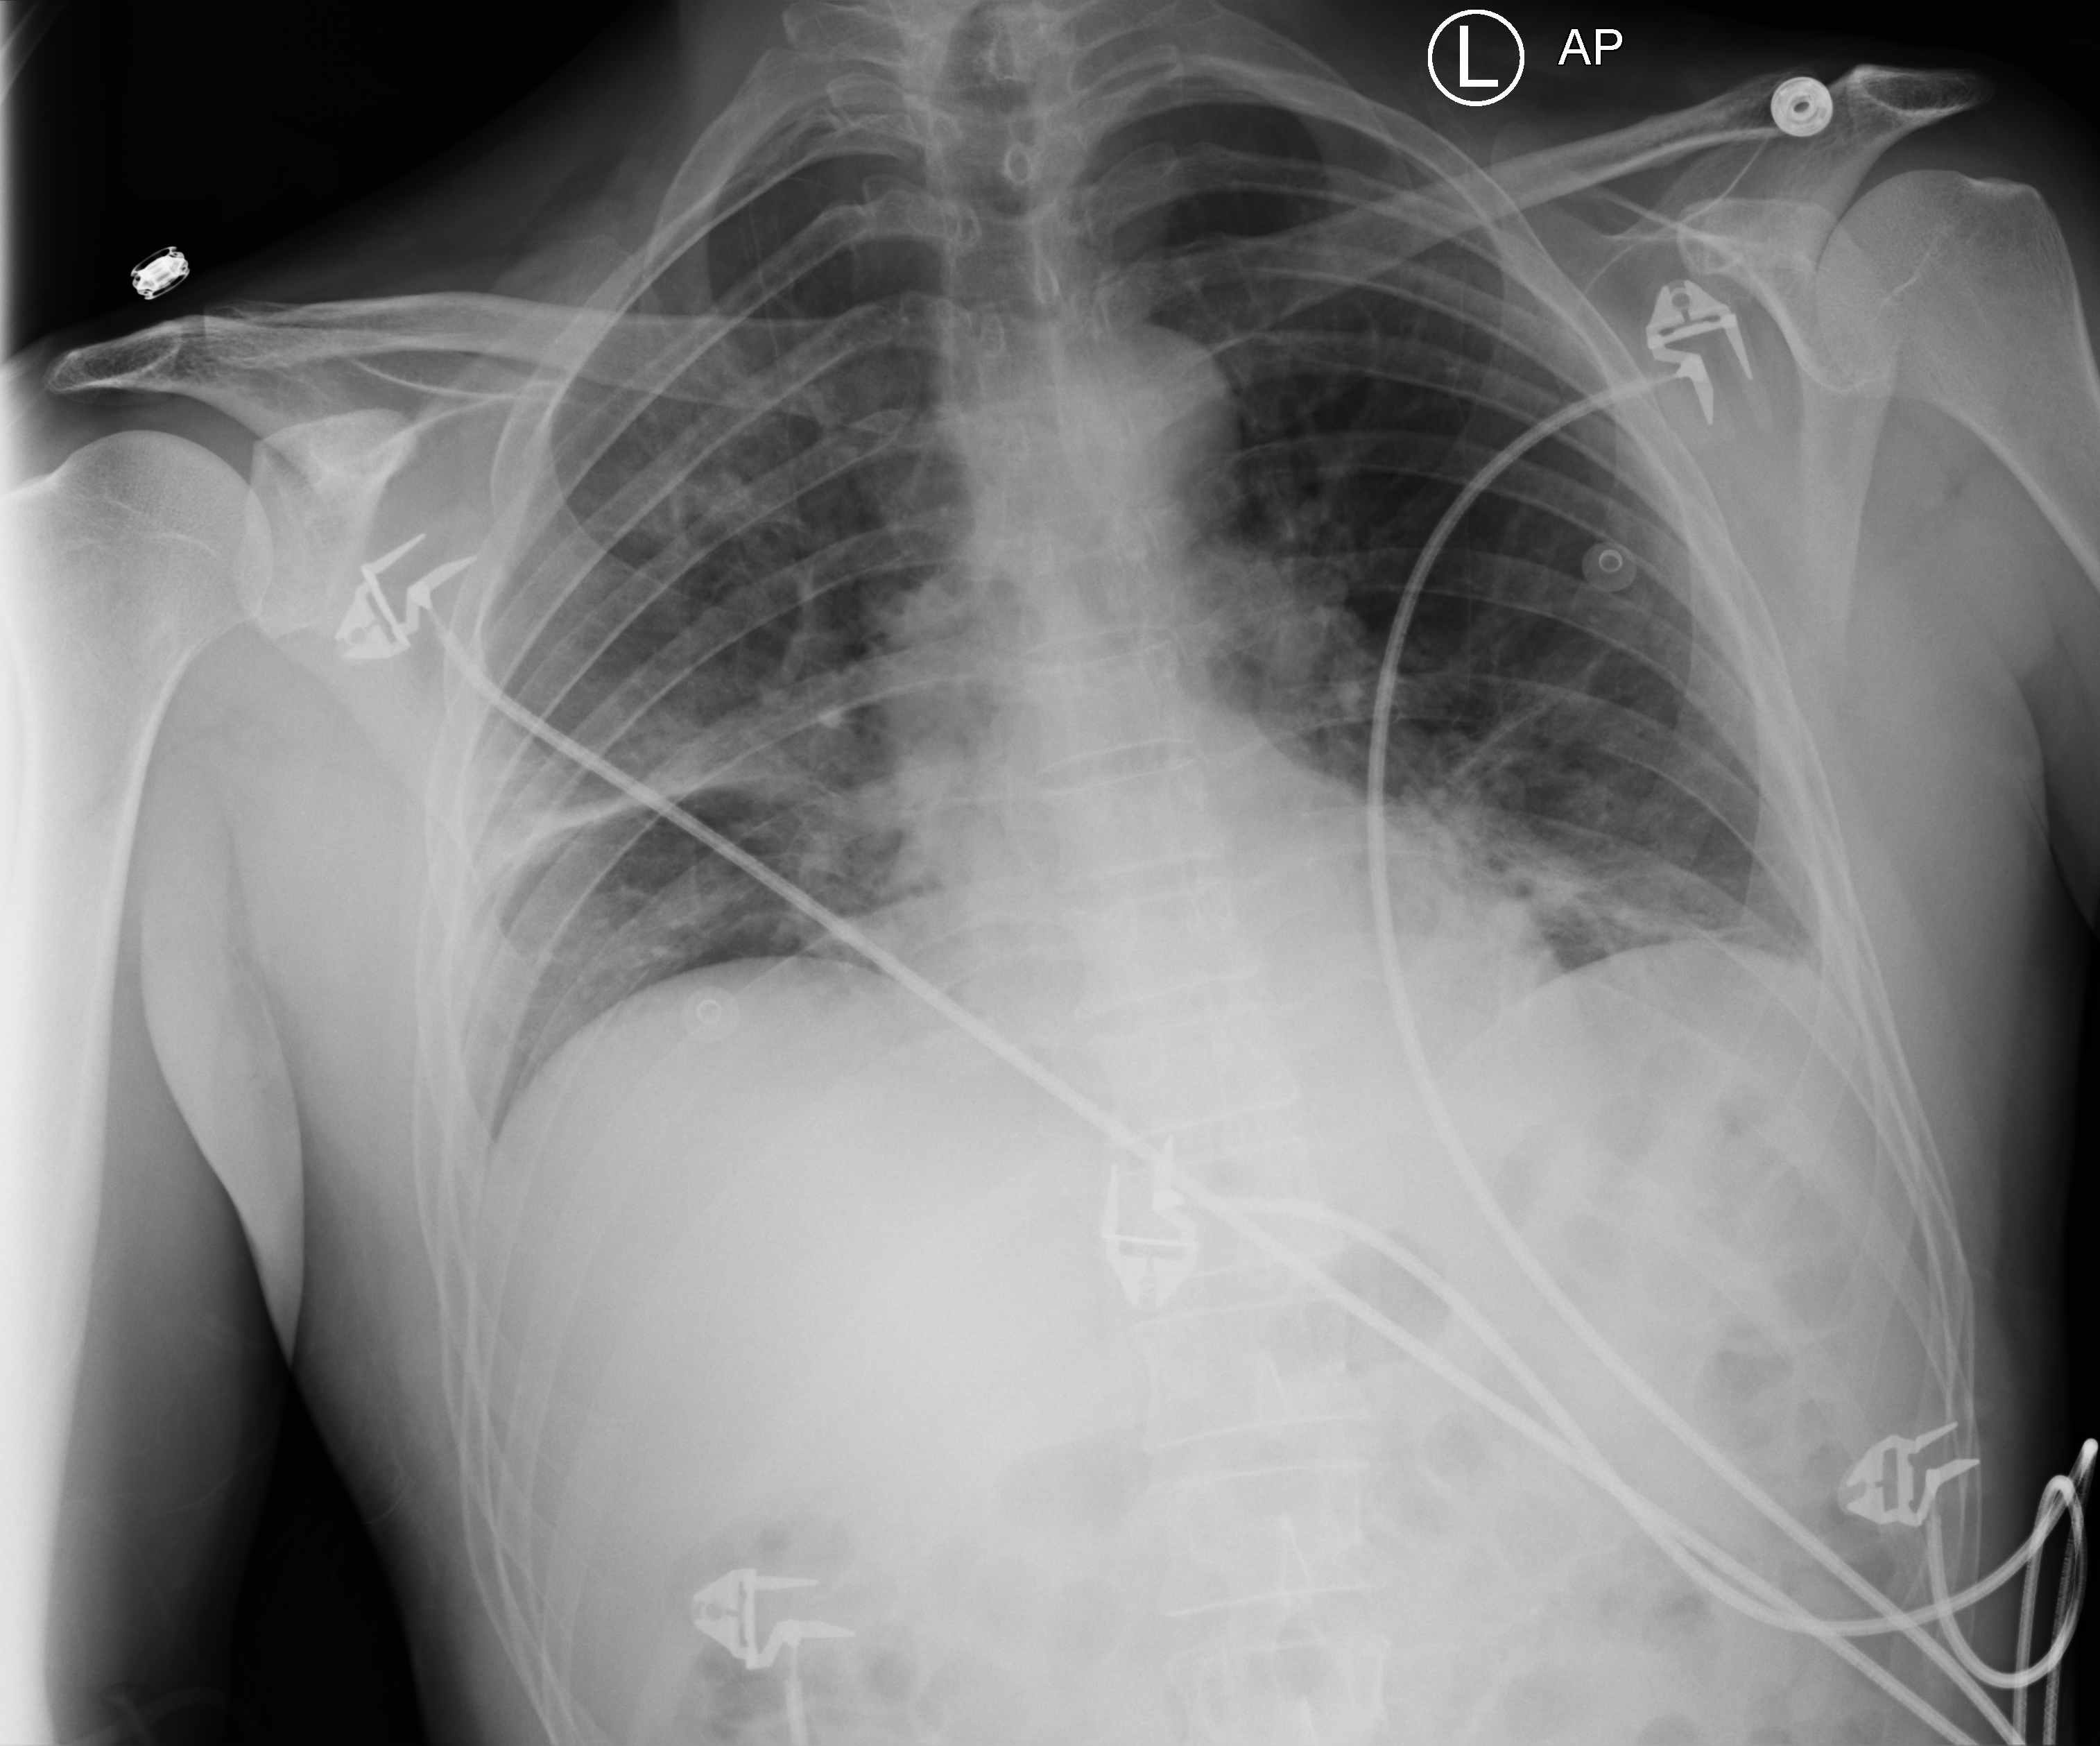
Bedside chest radiograph (computed radiography), anteroposterior (AP) projection. Male patient hospitalised with COVID-19, age 18–59 years.
Admission-level facts for this patient (not findings on this image; timing relative to this image not recorded): smoking status (admission record): never.